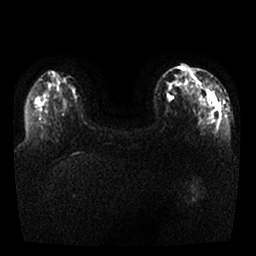
Breast MRI, one axial slice. Position 8 of 25 along the scan axis. Diffusion-weighted series; image 2 of 4 stored at this slice position (different b-values; order by instance number). 1.5 T. 4 mm slice thickness. 256 × 256 image matrix, field of view 340 × 340 mm. Female patient.
Annotated regions visible in this slice (expert manual segmentation):
- tumour on diffusion-weighted imaging: bounding box <181,68,222,129> (left, top, right, bottom; pixels)